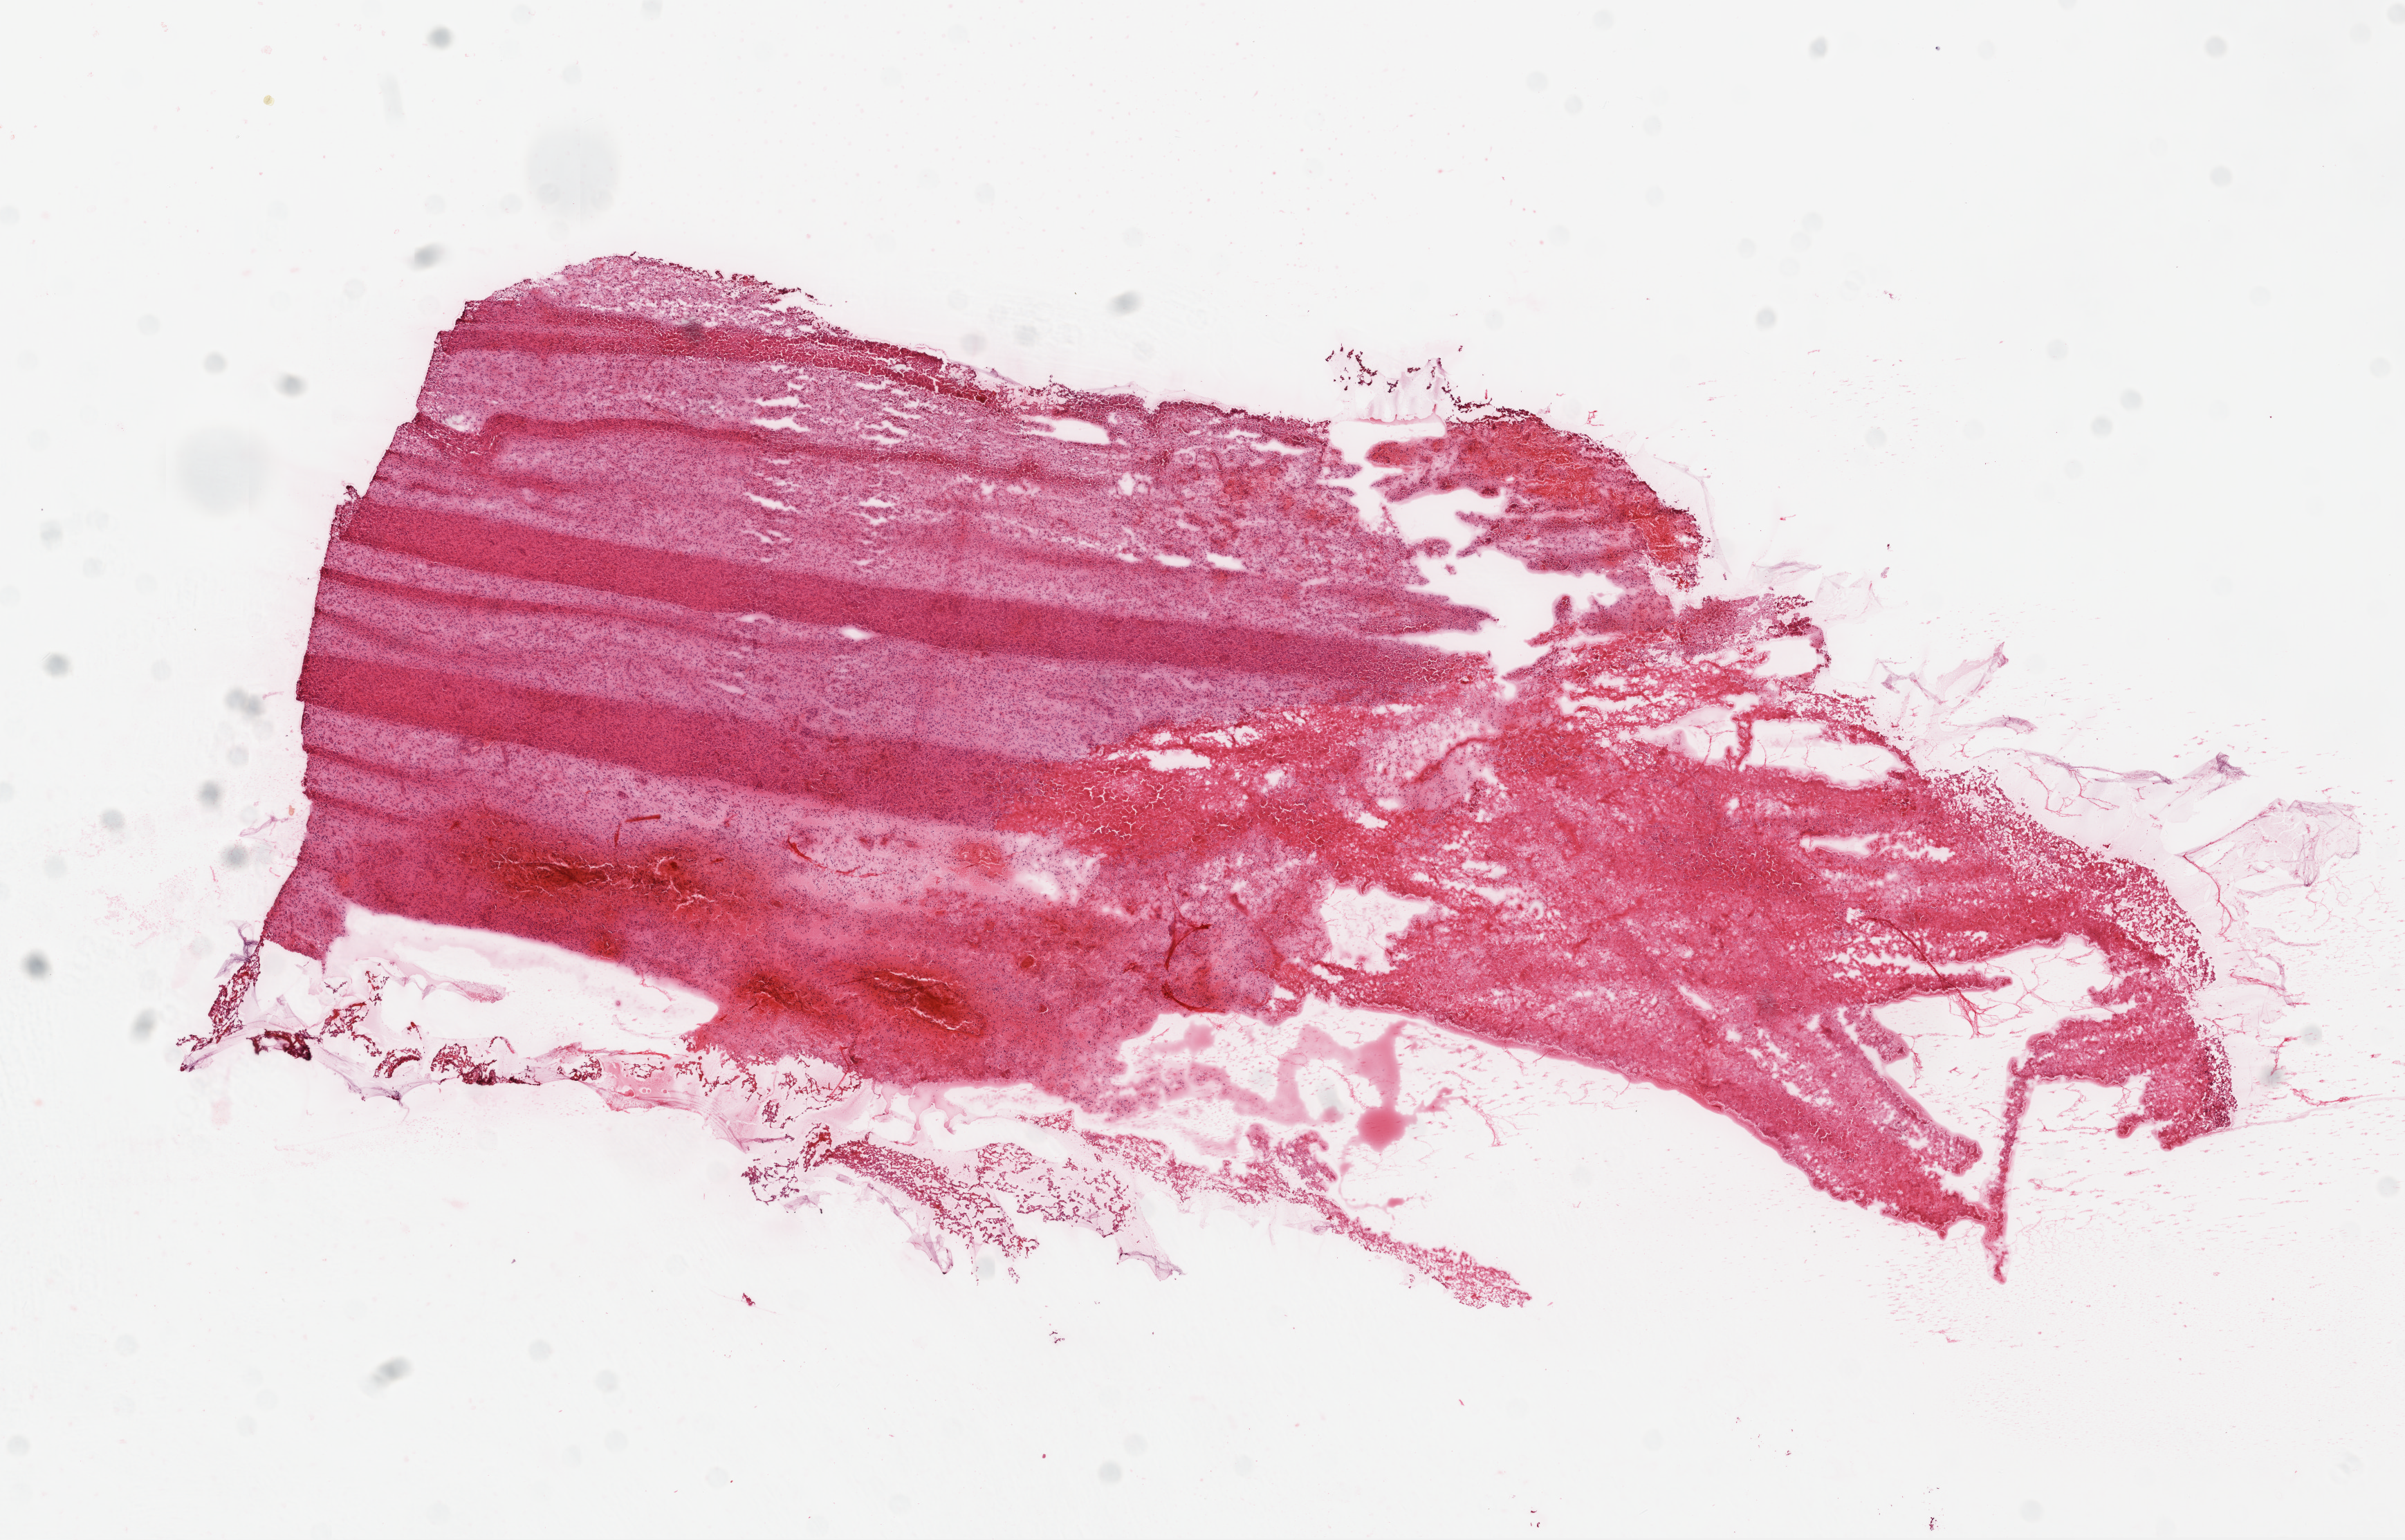
H&E whole-slide image, shown as a low-resolution overview of the whole scanned area (about 14.0 x 9.0 mm, slide scanned at 20x), frozen section, primary tumour sample from the brain. Patient: male, age at initial diagnosis 56 years. Slide review estimates, as recorded: tumour cells 70%, tumour nuclei 90%, stromal cells 10%, necrosis 20%.
• diagnosis: Glioblastoma